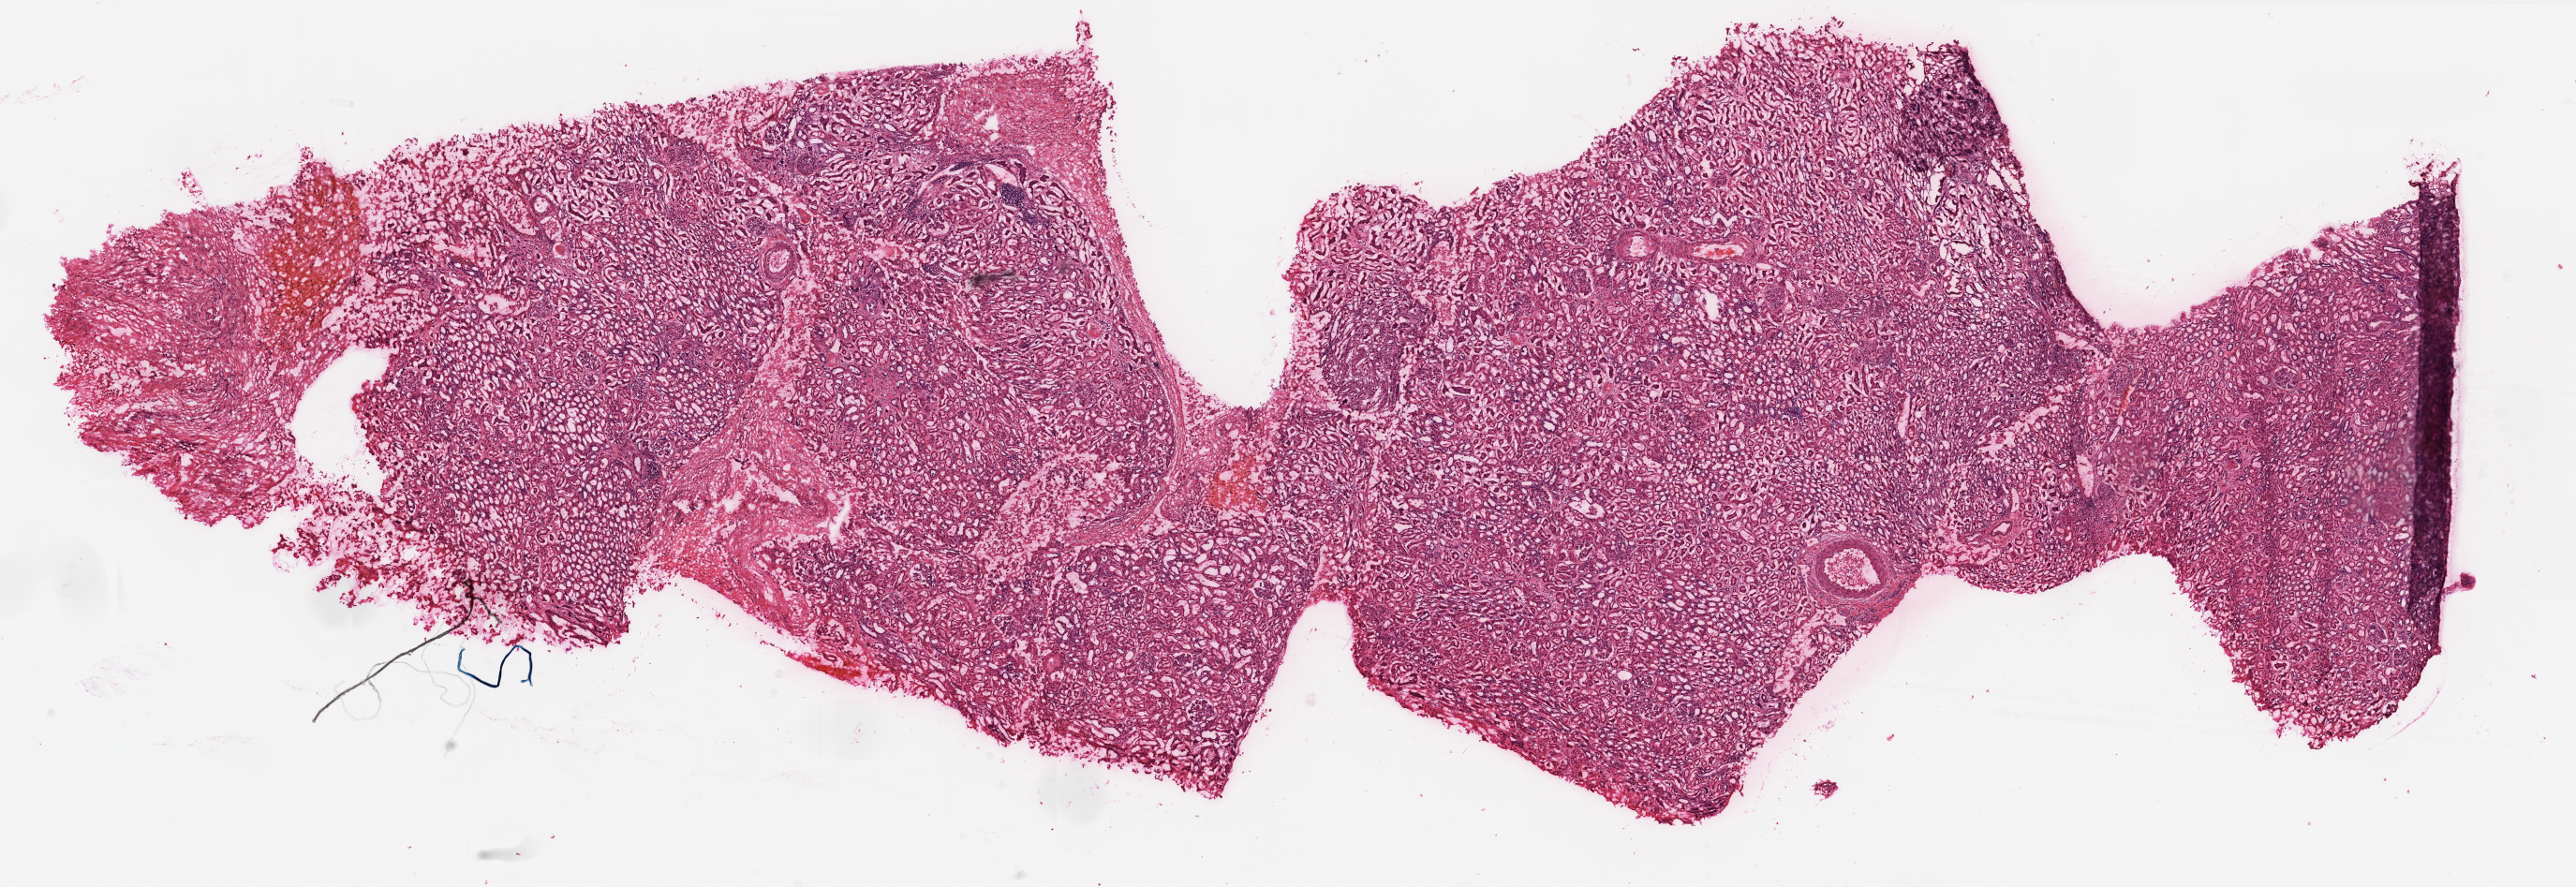
H&E-stained whole-slide image — a low-resolution overview of the entire scanned area, about 22.1 x 7.6 mm (acquisition: 20x scan). Frozen section from the top of the tissue portion. Kidney, solid tissue normal (non-tumour tissue) sample. Patient: male, age at initial diagnosis 64 years.
* this section: solid tissue normal (non-tumour) sample from the same patient
* patient diagnosis: Clear cell adenocarcinoma, NOS